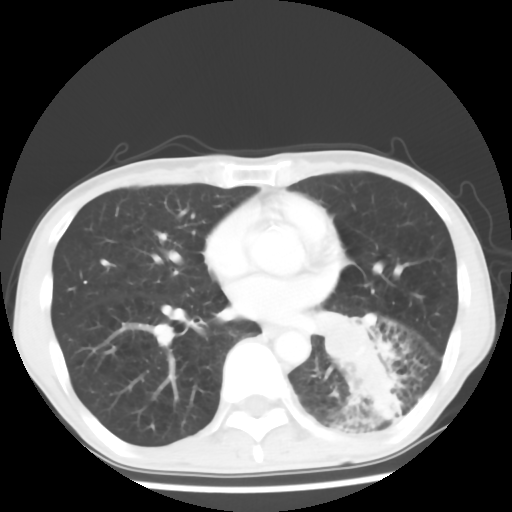
Chest CT, one axial slice. Position 28 of 64 along the scan axis. Reconstruction kernel STANDARD. 120 kVp. Lung window (W 1500 / L -600 HU). 5 mm slice thickness. 512 × 512 image matrix, field of view 313 × 313 mm. Patient: male, 68 years. From the clinical record (not read from this slice): clinical TNM (as recorded): T4 N0 M0.
Annotated regions visible in this slice (bounding box drawn by a radiologist):
- lung tumour (recorded histology: squamous cell carcinoma): bounding box (x1, y1, x2, y2) in pixels: (324, 310, 383, 376)